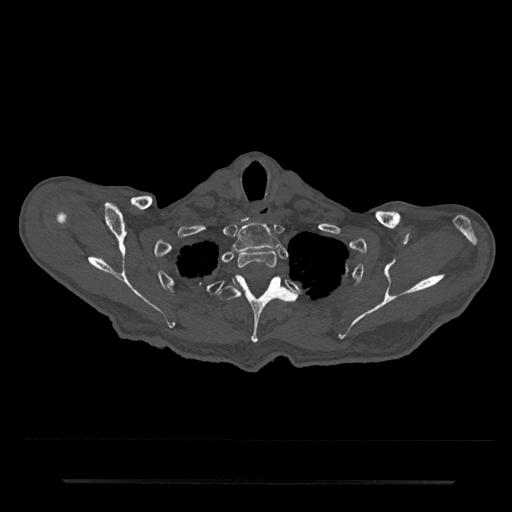
CT including the spine, one axial slice. Position 682 of 797 along the scan axis. Reconstruction kernel Br40s/3. 120 kVp. Bone window (W 1800 / L 400 HU). 0.5 mm slice thickness. 512 × 512 image matrix, field of view 427 × 427 mm. Male patient, age 74 years. From the clinical record (not read from this slice): primary cancer: prostate.
Outlined on this slice (semi-automatically segmented with operator editing):
- T1 vertebra: box from (x=232, y=223) to (x=280, y=252) px
- T2 vertebra: (x=238, y=250)–(x=277, y=269)
- T3 vertebra: (x=217, y=275)–(x=296, y=344)